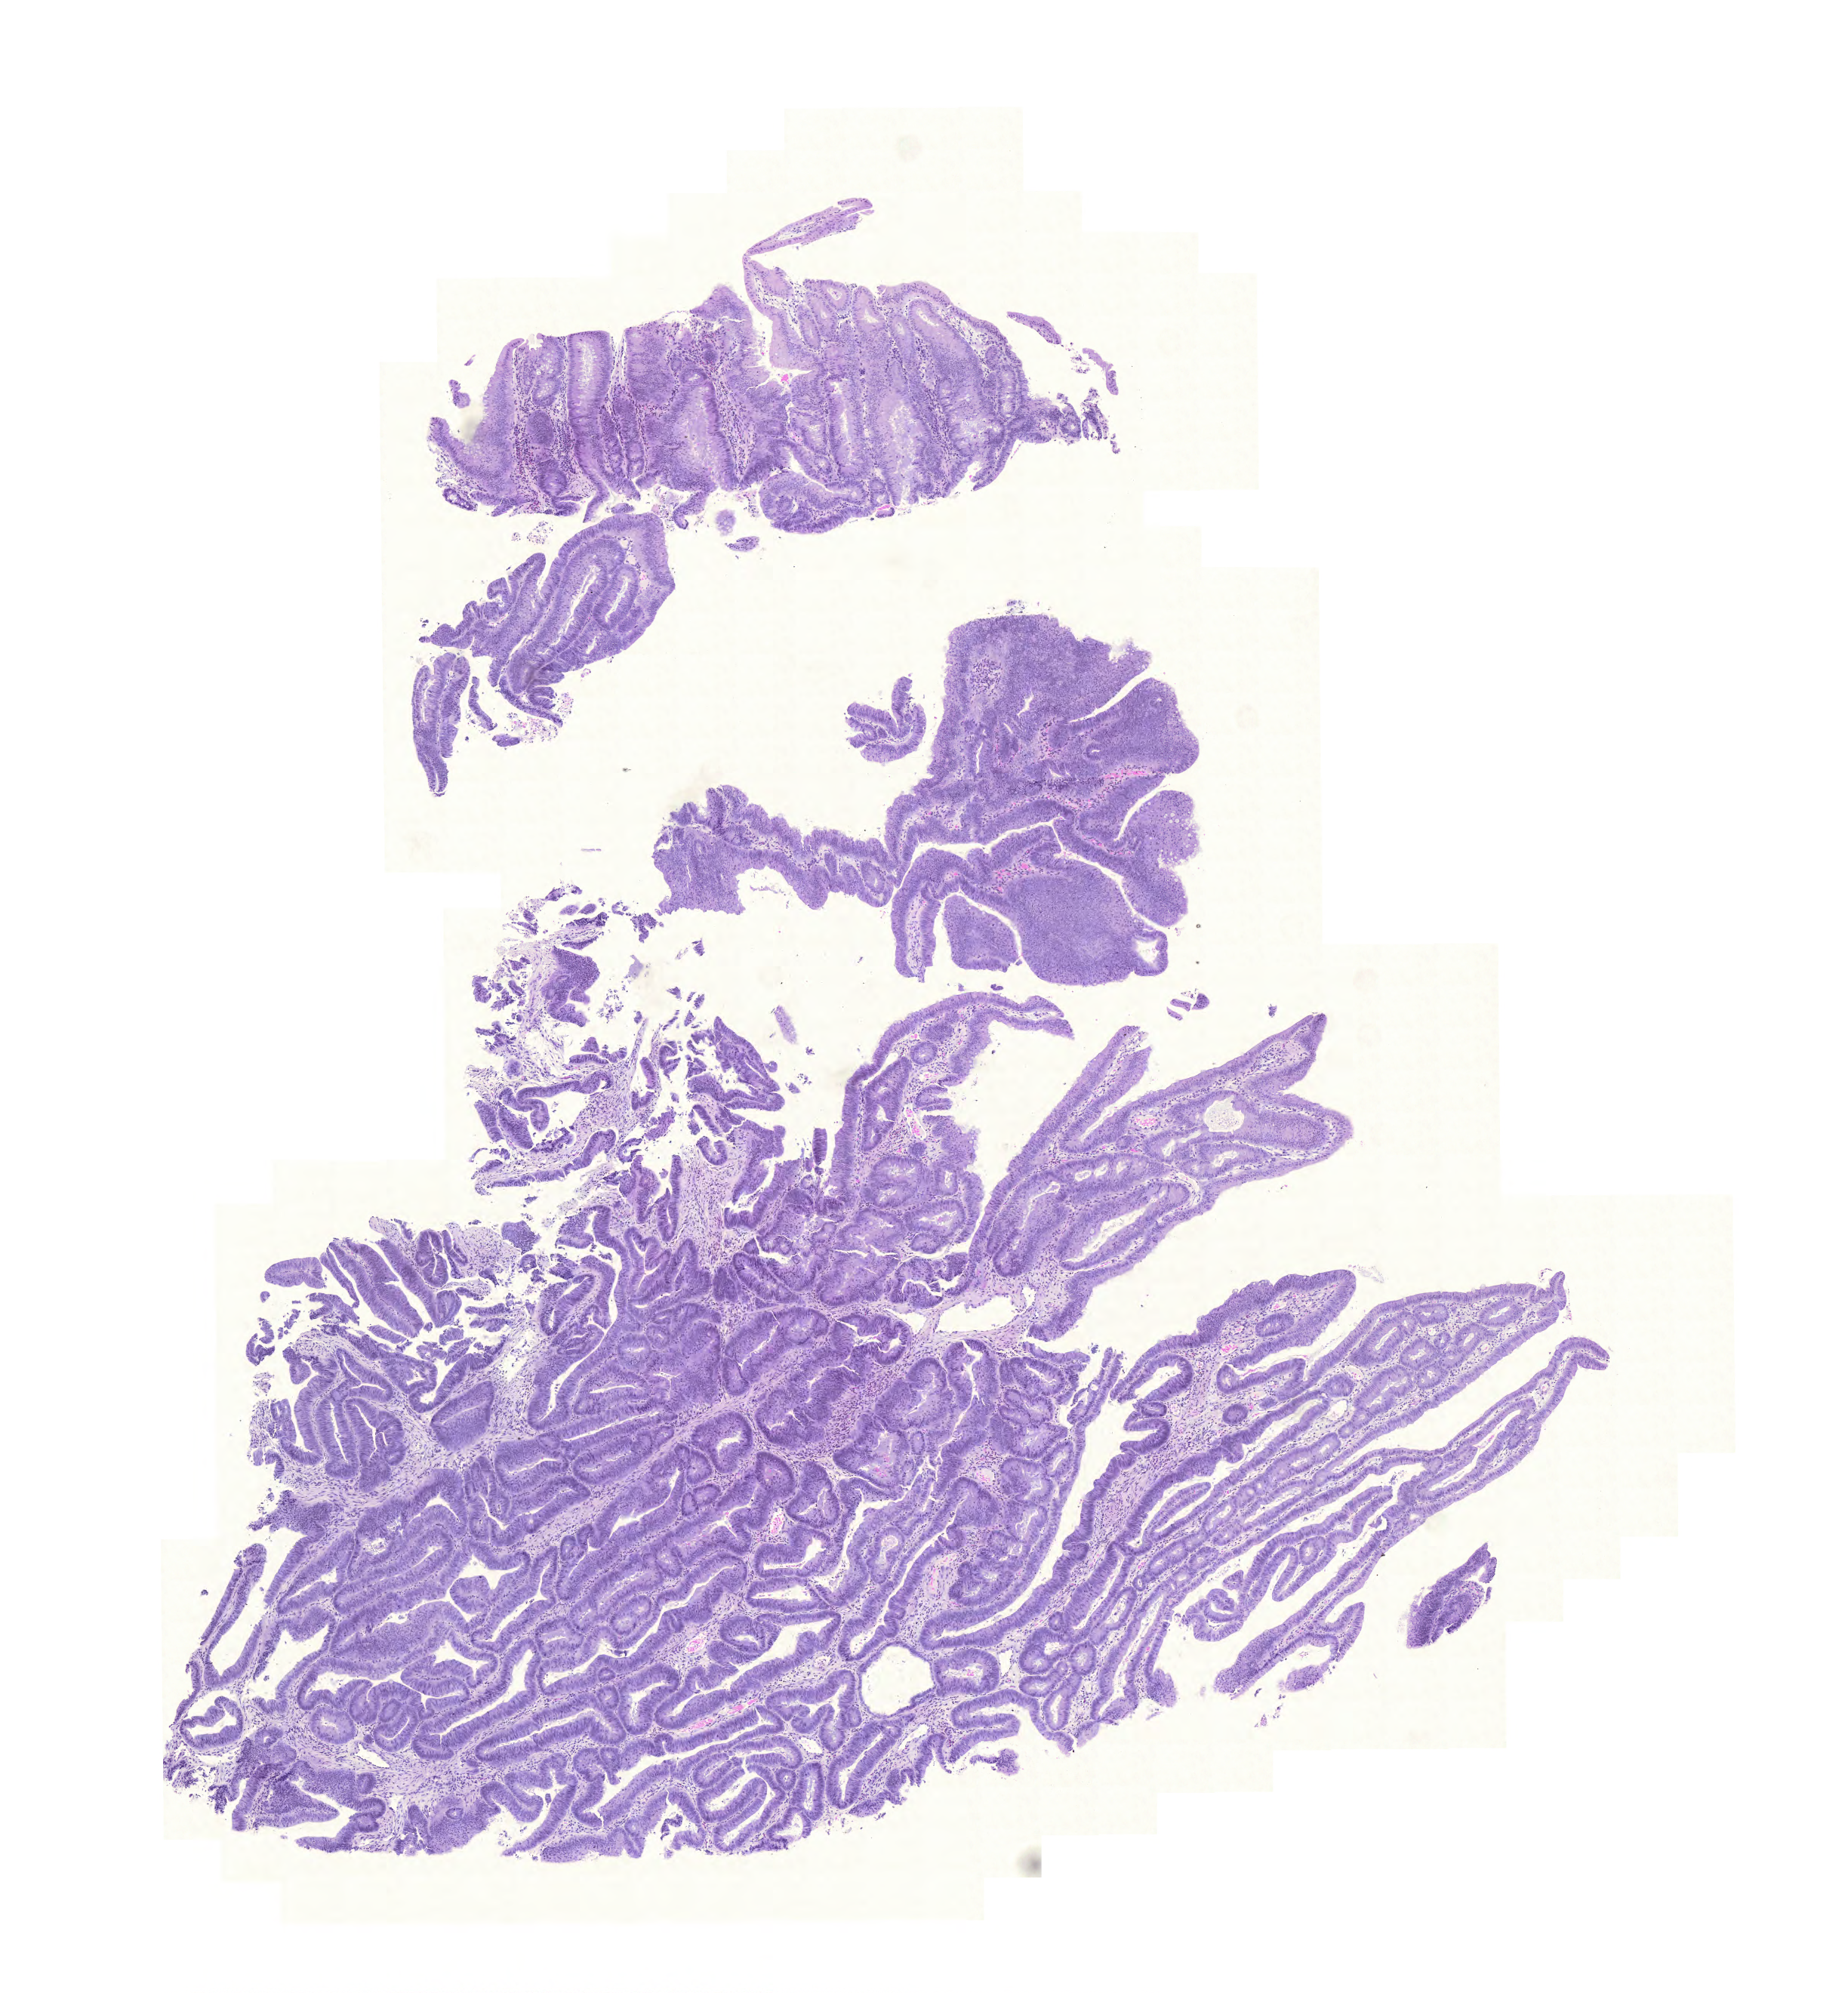
Digitized H&E-stained tissue section (whole slide) — a low-resolution overview of the entire scanned area, about 9.1 x 9.8 mm (from a 20x scan). FFPE section. Colon, primary tumour sample. Patient: female, age at initial diagnosis 75 years.
Pathologic diagnosis: Adenocarcinoma, NOS (sigmoid colon).